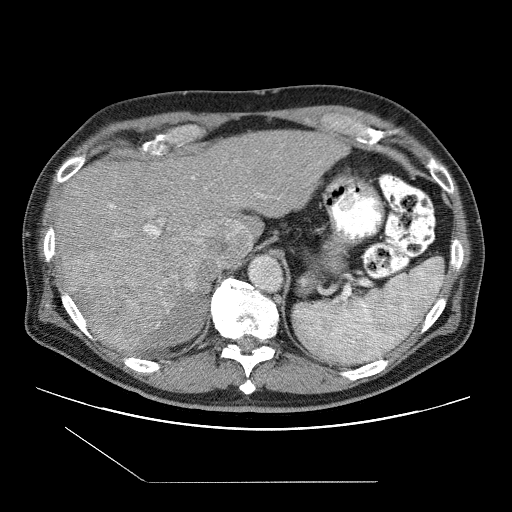
Contrast-enhanced abdominal CT (liver protocol), one axial slice. Position 73 of 109 along the scan axis. 120 kVp. One of 2 acquisitions stored at this slice position. Soft-tissue window (W 400 / L 40 HU). 2.5 mm slice thickness. 512 × 512 image matrix, field of view 400 × 400 mm. From the clinical record (not read from this slice): diagnosis: hepatocellular carcinoma (patient treated with transarterial chemoembolisation; whether this scan precedes or follows treatment is not stated here); TNM stage (as recorded): Stage-IIIB; Child-Pugh class: A; tumour differentiation: well differentiated; tumour nodularity: multinodular.
Structures marked on this image (semi-automatically segmented with operator editing):
- liver parenchyma outside the tumour (the mass and vessels are separate outlines, so this box may not span the whole liver): bounding box <54,130,346,350> (left, top, right, bottom; pixels)
- mass: <61,245,197,350>
- liver vessels: <110,177,244,241>